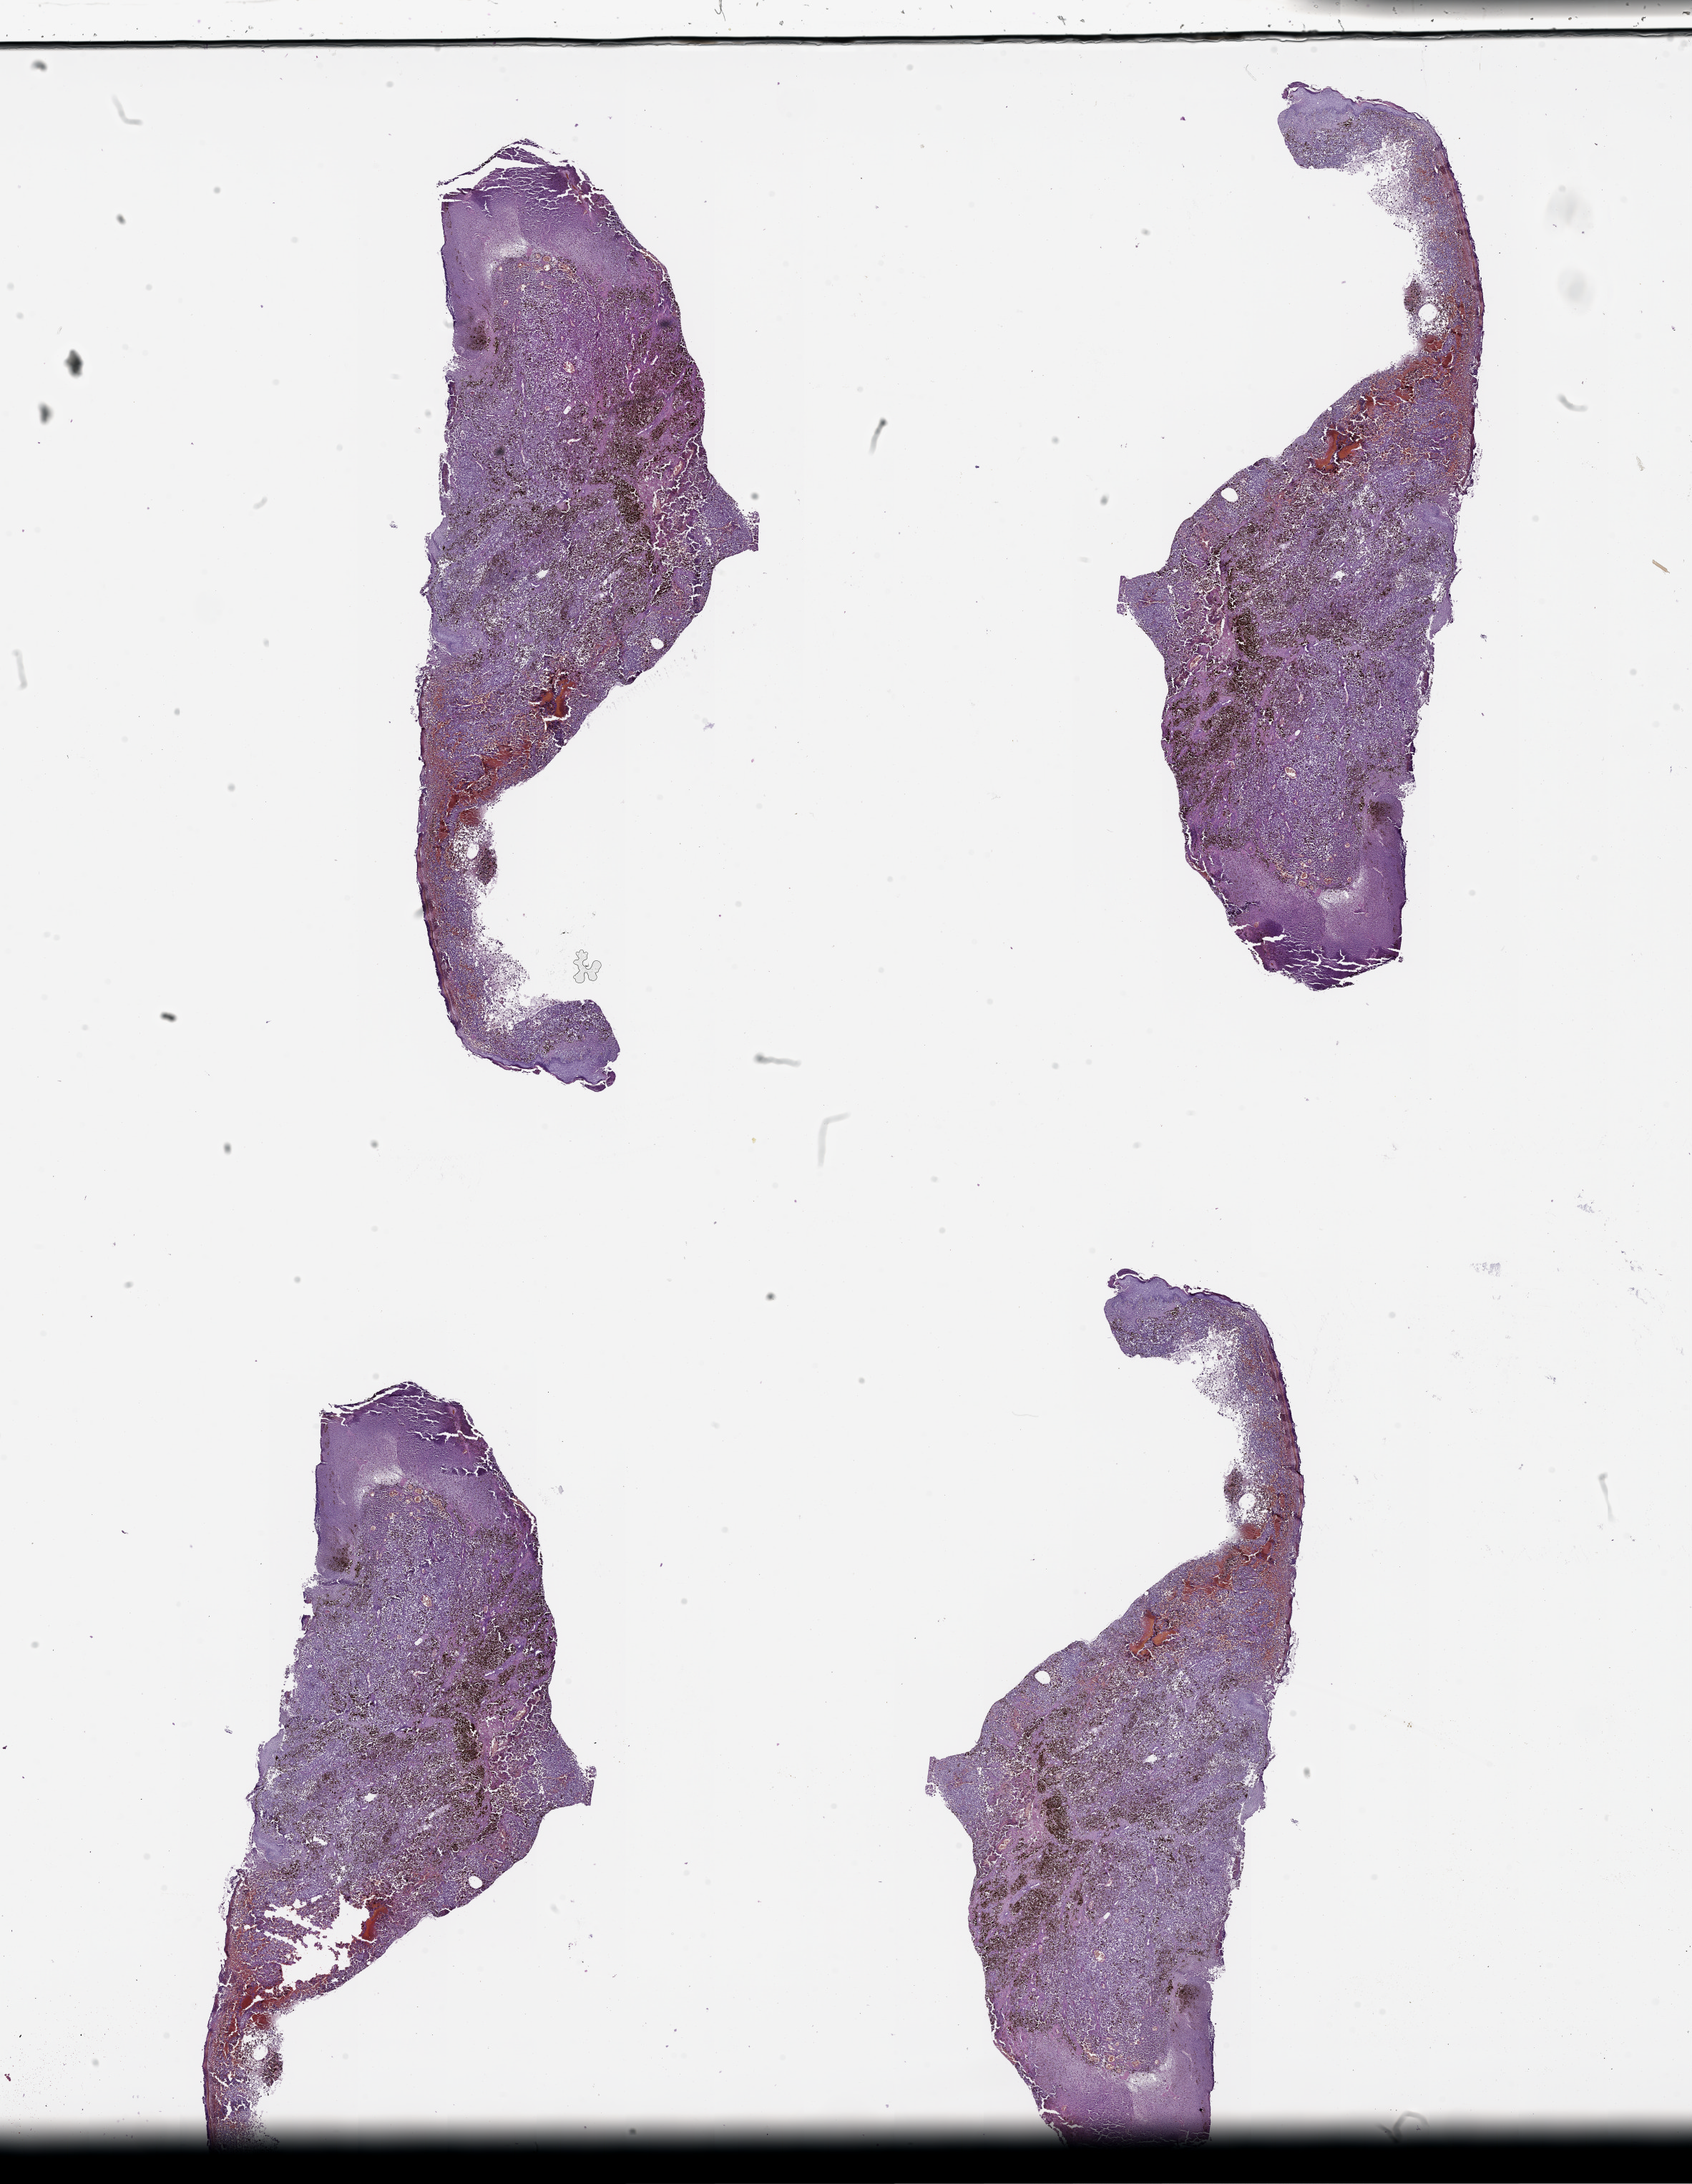
Digitized H&E-stained tissue section (whole slide), low-resolution overview of the scanned area, about 19.0 x 24.6 mm (slide scanned at 20x), tumour tissue sample, sampled site: trunk. 81-year-old female patient. Slide review estimates, as recorded: tumour nuclei 80%, necrosis 0%.
- AJCC pathologic stage: IIC
- diagnosis: Malignant melanoma, NOS
- primary tumour site (as recorded): trunk